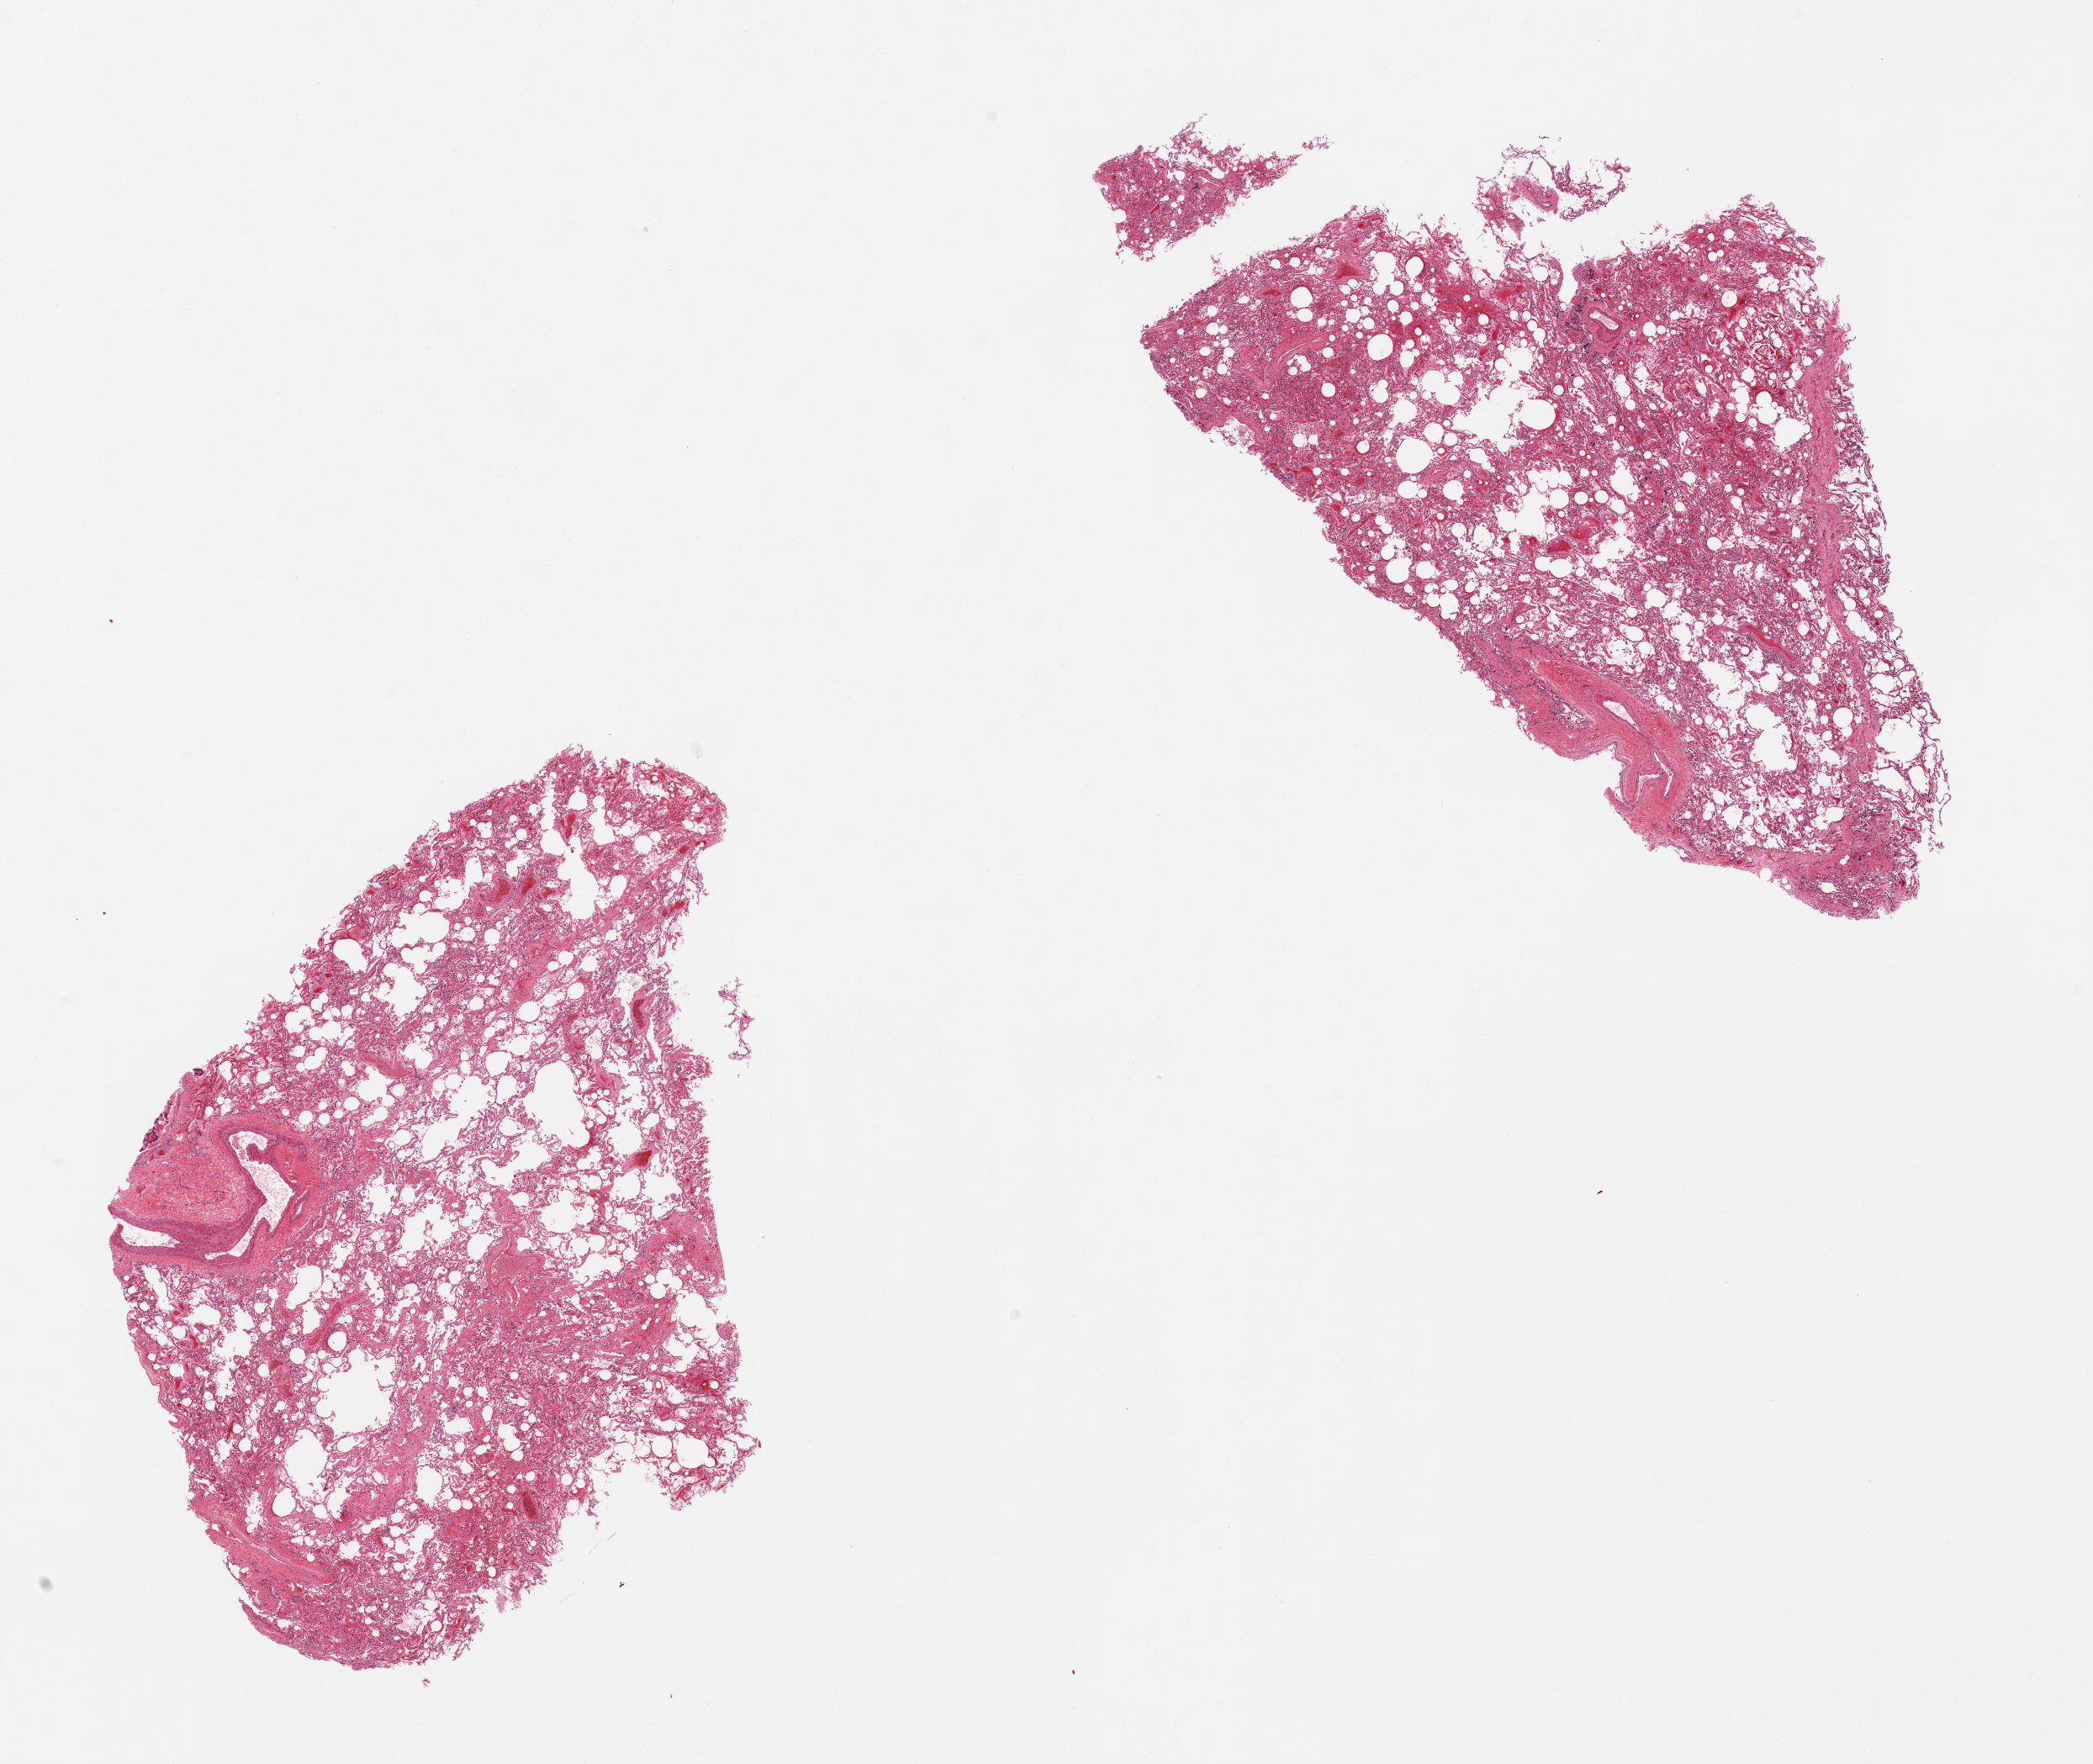
Haematoxylin and eosin whole-slide image — whole scanned area (about 19.7 x 16.6 mm) shown as a low-resolution overview; PAXgene-fixed paraffin-embedded (PFPE) section; sampled site (target tissue): lung; tissue donor sample. Male donor.
- reviewer comment on this tissue sample: 2 pieces, mild fibrosis, some hemosiderin-laden macrophages